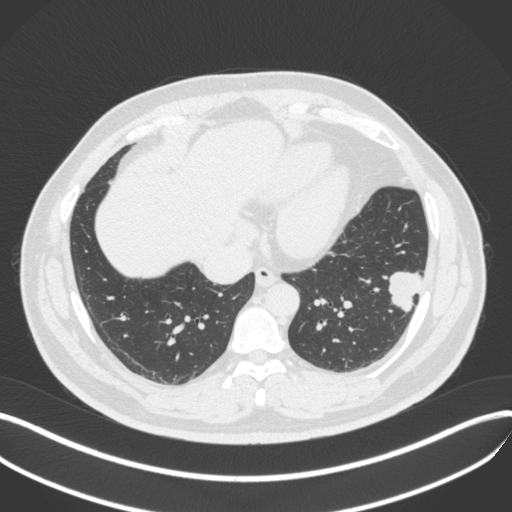
Chest CT, one axial slice; slice 134 of 420 in the series (ordered by position); lung window (W 1500 / L -600 HU); 512 × 512 image matrix, field of view 400 × 400 mm. Patient: male, 39 years. Case-level facts recorded for this patient, not image findings: clinical TNM (as recorded): T2a N0 M0.
Annotated regions visible in this slice (bounding box drawn by a radiologist):
- lung tumour (recorded histology: adenocarcinoma): box from (x=383, y=267) to (x=428, y=315) px